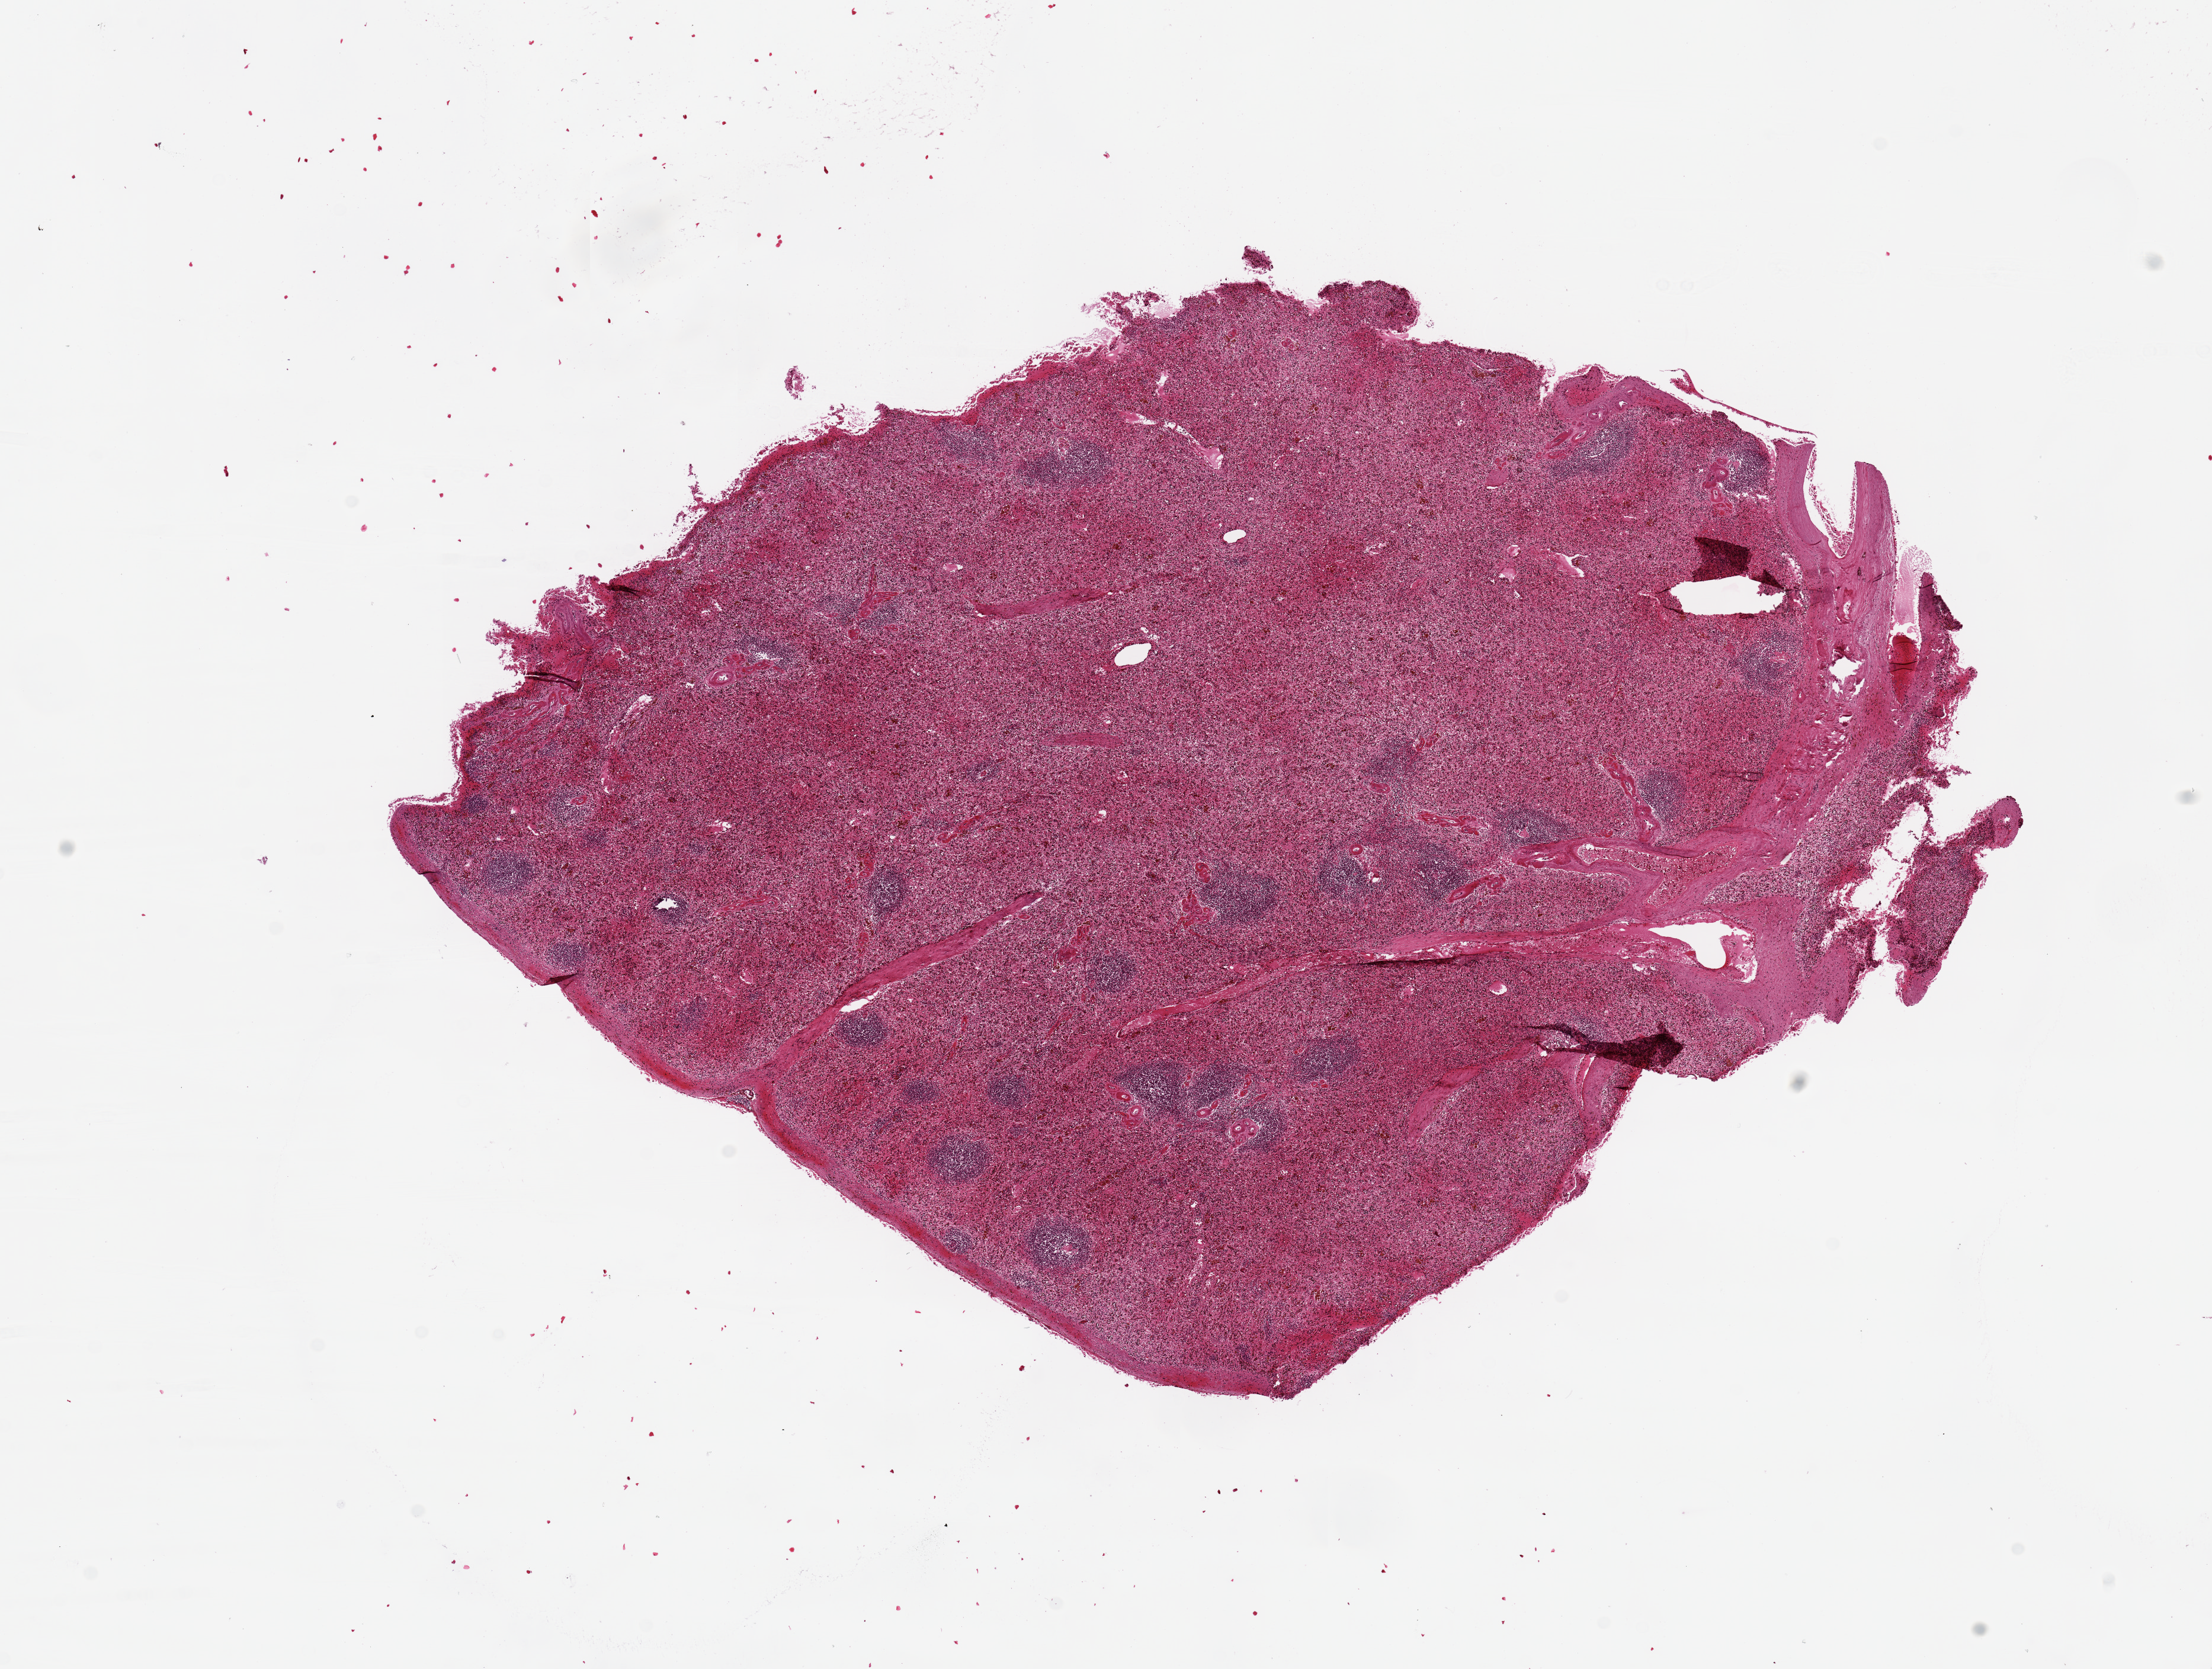
Digitized haematoxylin and eosin-stained section, low-resolution overview of the scanned area, about 14.8 x 11.1 mm (from a 20x scan); PAXgene-fixed, paraffin-embedded tissue; target tissue: spleen; donor tissue sample. Donor sex: female.
Reviewer comment on this tissue sample: Mild autolysis (???score 1???).